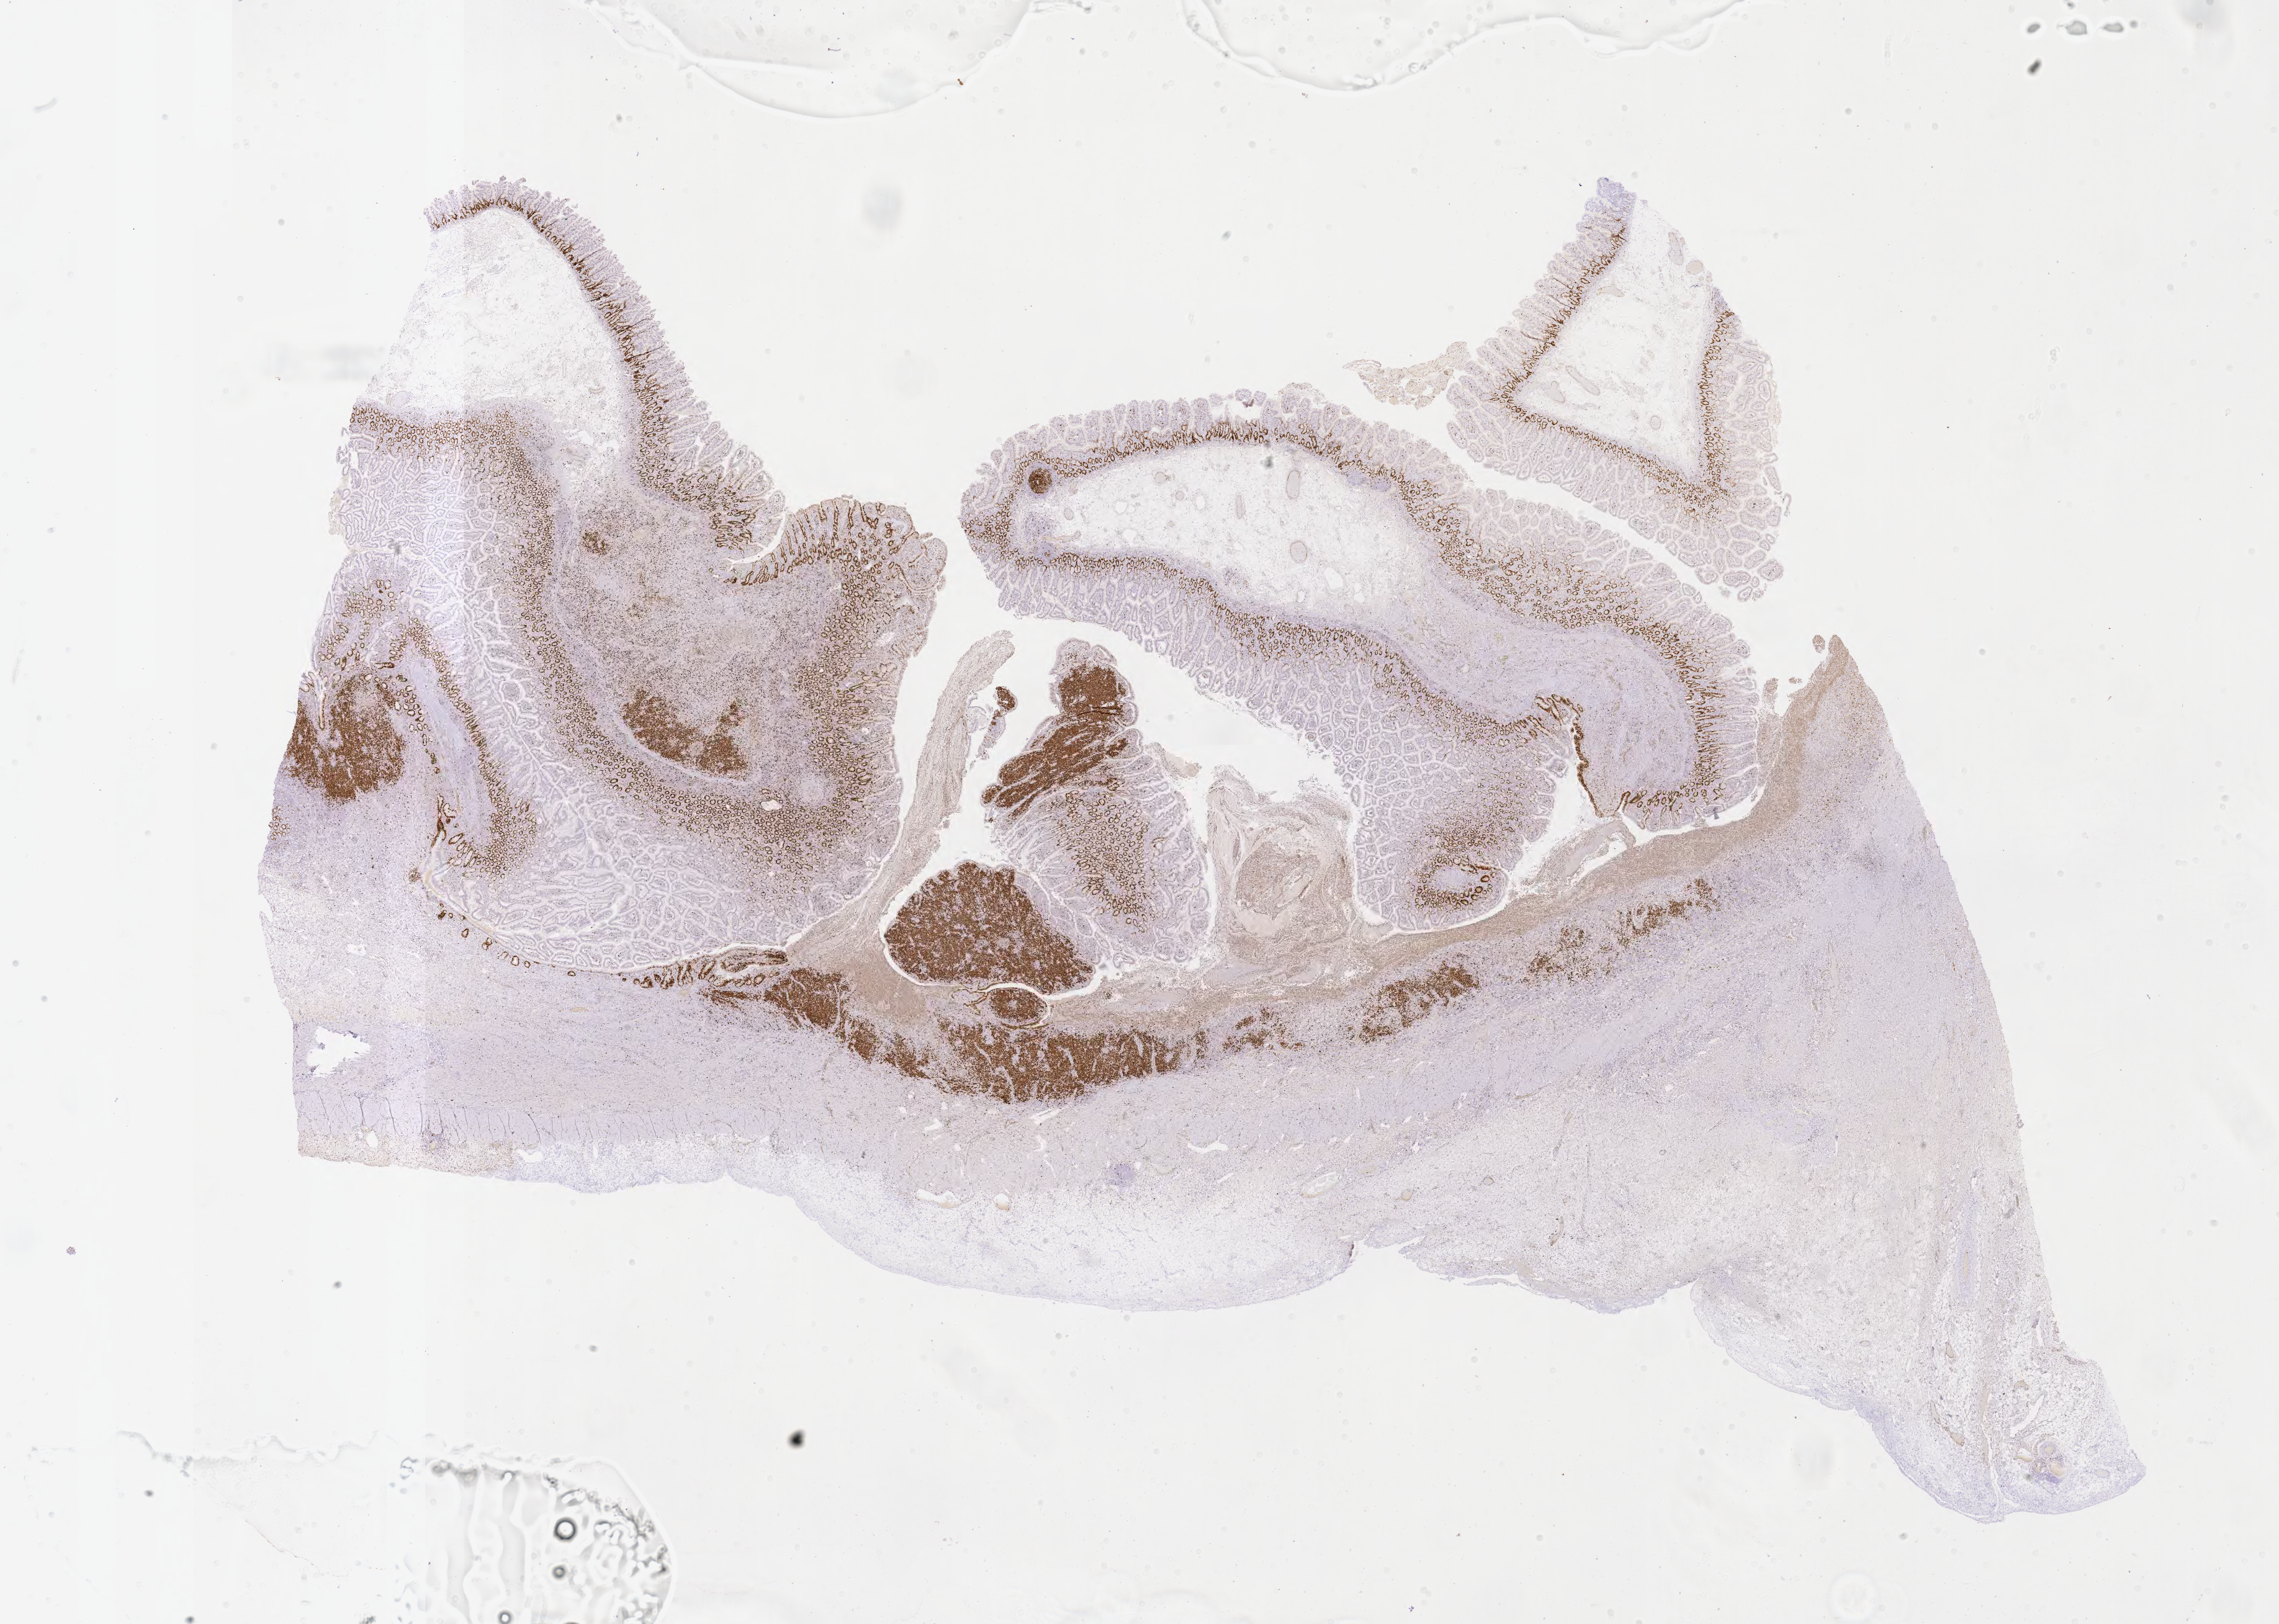
IHC for Ki-67, whole-slide image, low-resolution overview of the scanned area, about 29.7 x 21.1 mm; tumor tissue. Female patient, aged 44.
Histologic diagnosis: Burkitt lymphoma, NOS.